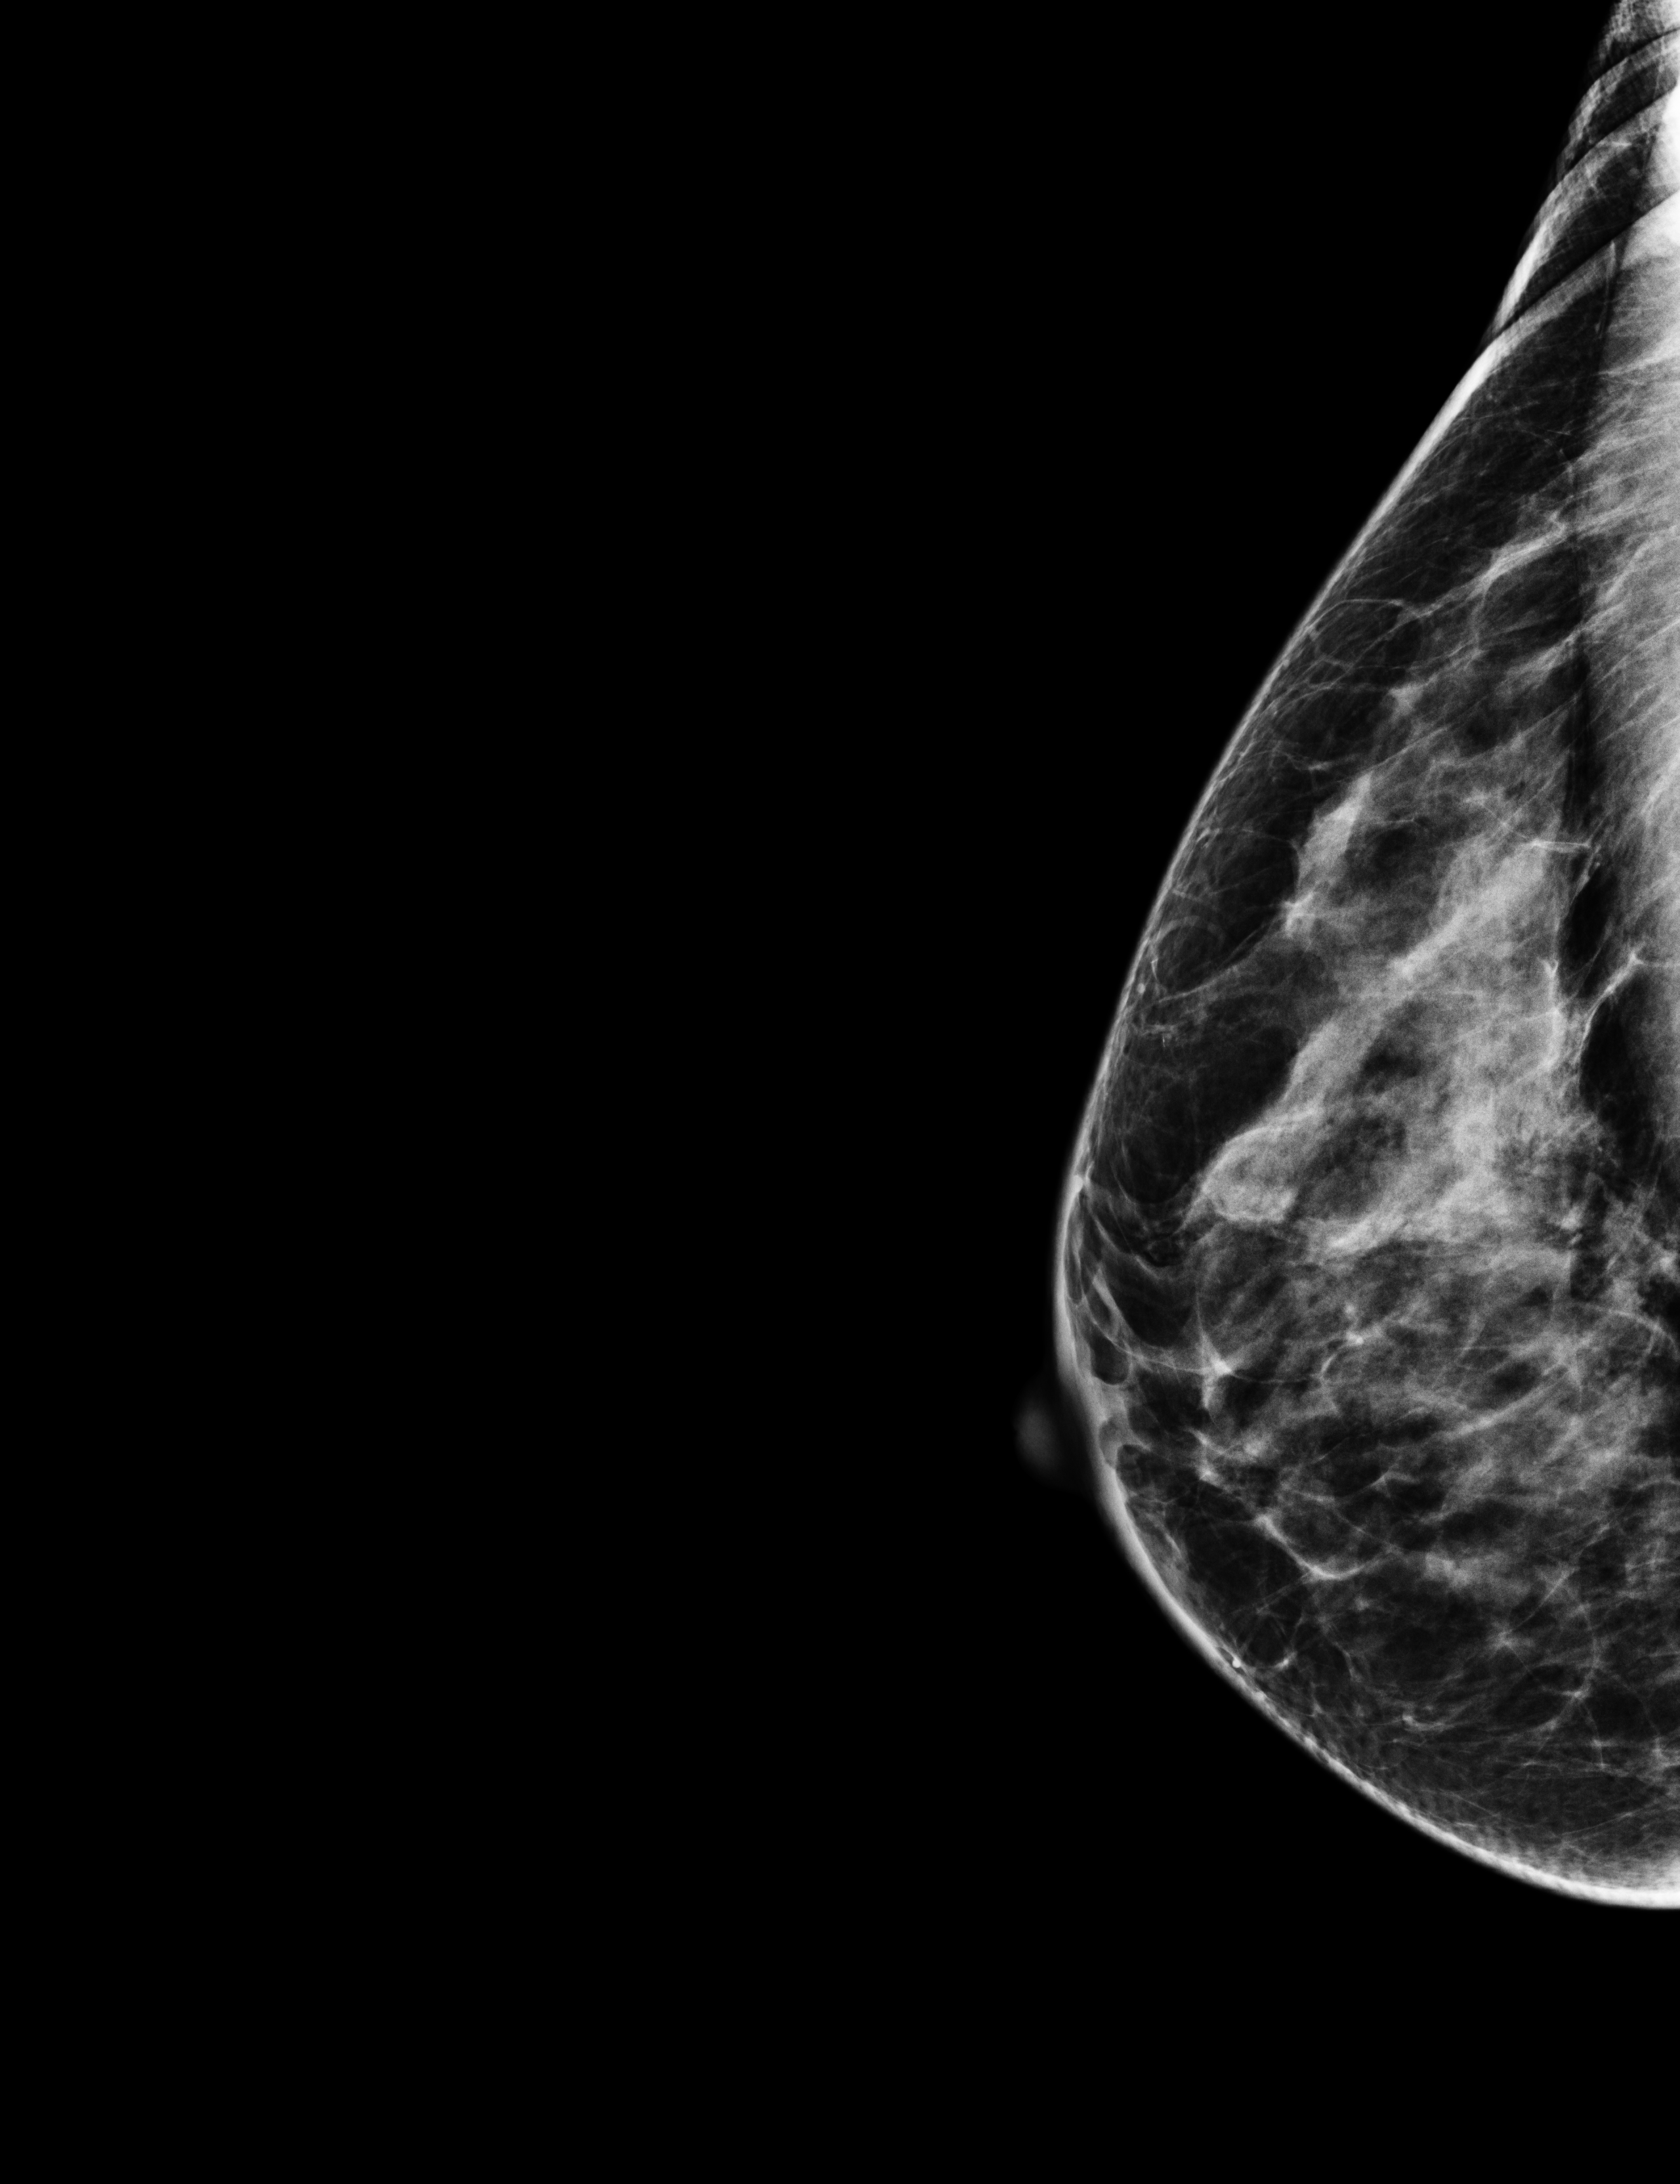
Screening examination, compressed breast thickness 48 mm, system: Selenia Dimensions. Patient: female, 53 years.
Image type: full-field digital mammogram. Breast: right. Projection: laterally exaggerated craniocaudal (XCCL) view.